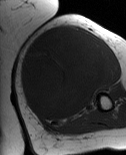
MRI of an extremity soft-tissue mass, one axial slice. Position 40 of 86 along the scan axis. MR volume resampled by the dataset authors to the PET/CT grid (not the native acquisition matrix). 3.27 mm slice thickness. 126 × 155 image matrix, field of view 123 × 151 mm. Female patient. Case-level facts recorded for this patient, not image findings: histological type: pleiomorphic leiomyosarcoma; grade: high; site of the primary tumour: left biceps.
Annotated regions visible in this slice (expert contour drawn on MRI and transferred to this co-registered scan by the dataset authors):
- gross tumour volume including surrounding oedema: bounding box <20,26,108,121> (left, top, right, bottom; pixels)
- gross tumour volume (mass): <20,26,108,121>